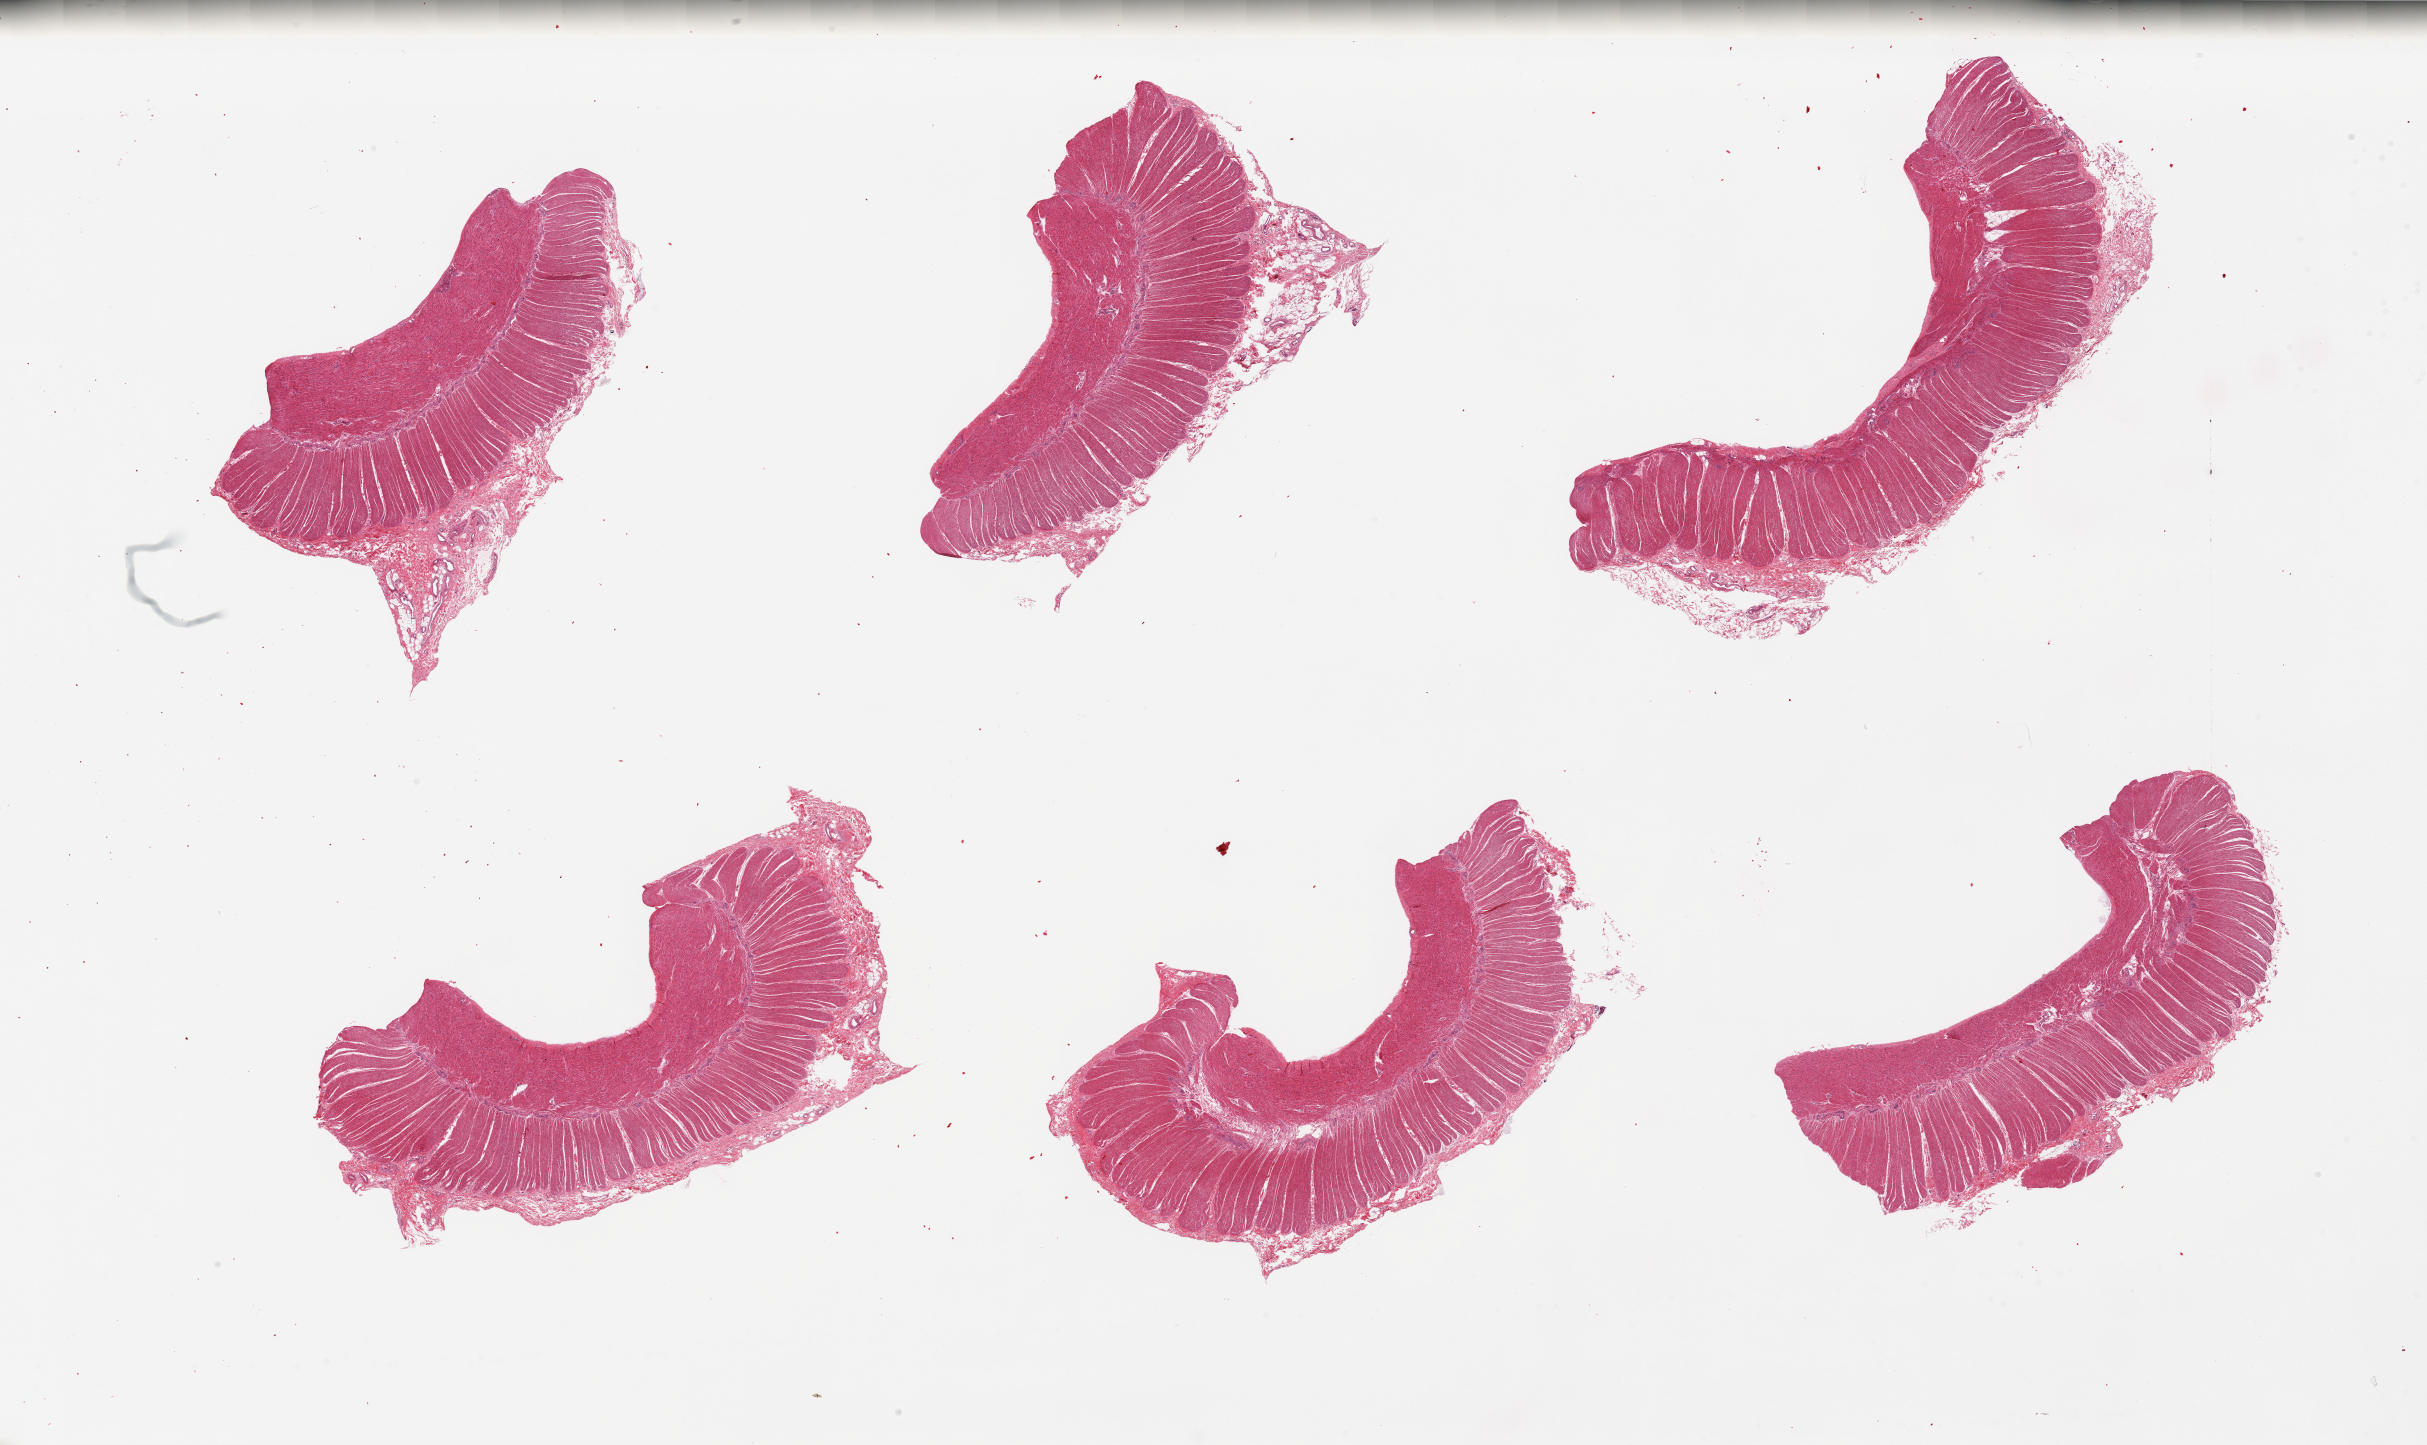
Hematoxylin and eosin (H&E) whole-slide image, whole scanned area (about 38.4 x 22.9 mm, from a 20x scan) shown as a low-resolution overview. PAXgene-fixed, paraffin-embedded tissue. Section of sigmoid colon (target tissue). Donor tissue sample. Donor: male.
Pathologist's review note for this sample: 6 pieces. Well dissected muscle with focally adherent submucosa.